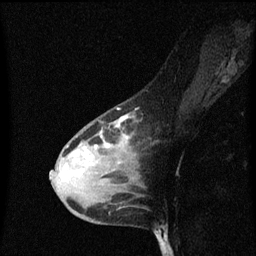
Breast MRI (dynamic contrast-enhanced), one sagittal slice; slice 41 of 60 in the series (ordered by position); dynamic contrast-enhanced series, image 2 of 3 at this slice position (ordered by acquisition); 1.5 T; TE 4.2 ms, TR 8.4 ms; 256 × 256 image matrix, field of view 200 × 200 mm. Patient: female, 38 years. Case-level facts recorded for this patient, not image findings: setting: breast cancer imaged before/during neoadjuvant chemotherapy; receptor status: HR-positive, HER2-negative.
Structures marked on this image (semi-automatic segmentation, software-assisted and operator-edited):
- analysis volume of interest (the breast-tissue region the enhancement analysis was run in; not a lesion): bounding box <50,108,141,205> (left, top, right, bottom; pixels)
- tumour enhancement mask (voxels above the 70 % enhancement threshold inside the analysis volume of interest): <62,116,129,179>